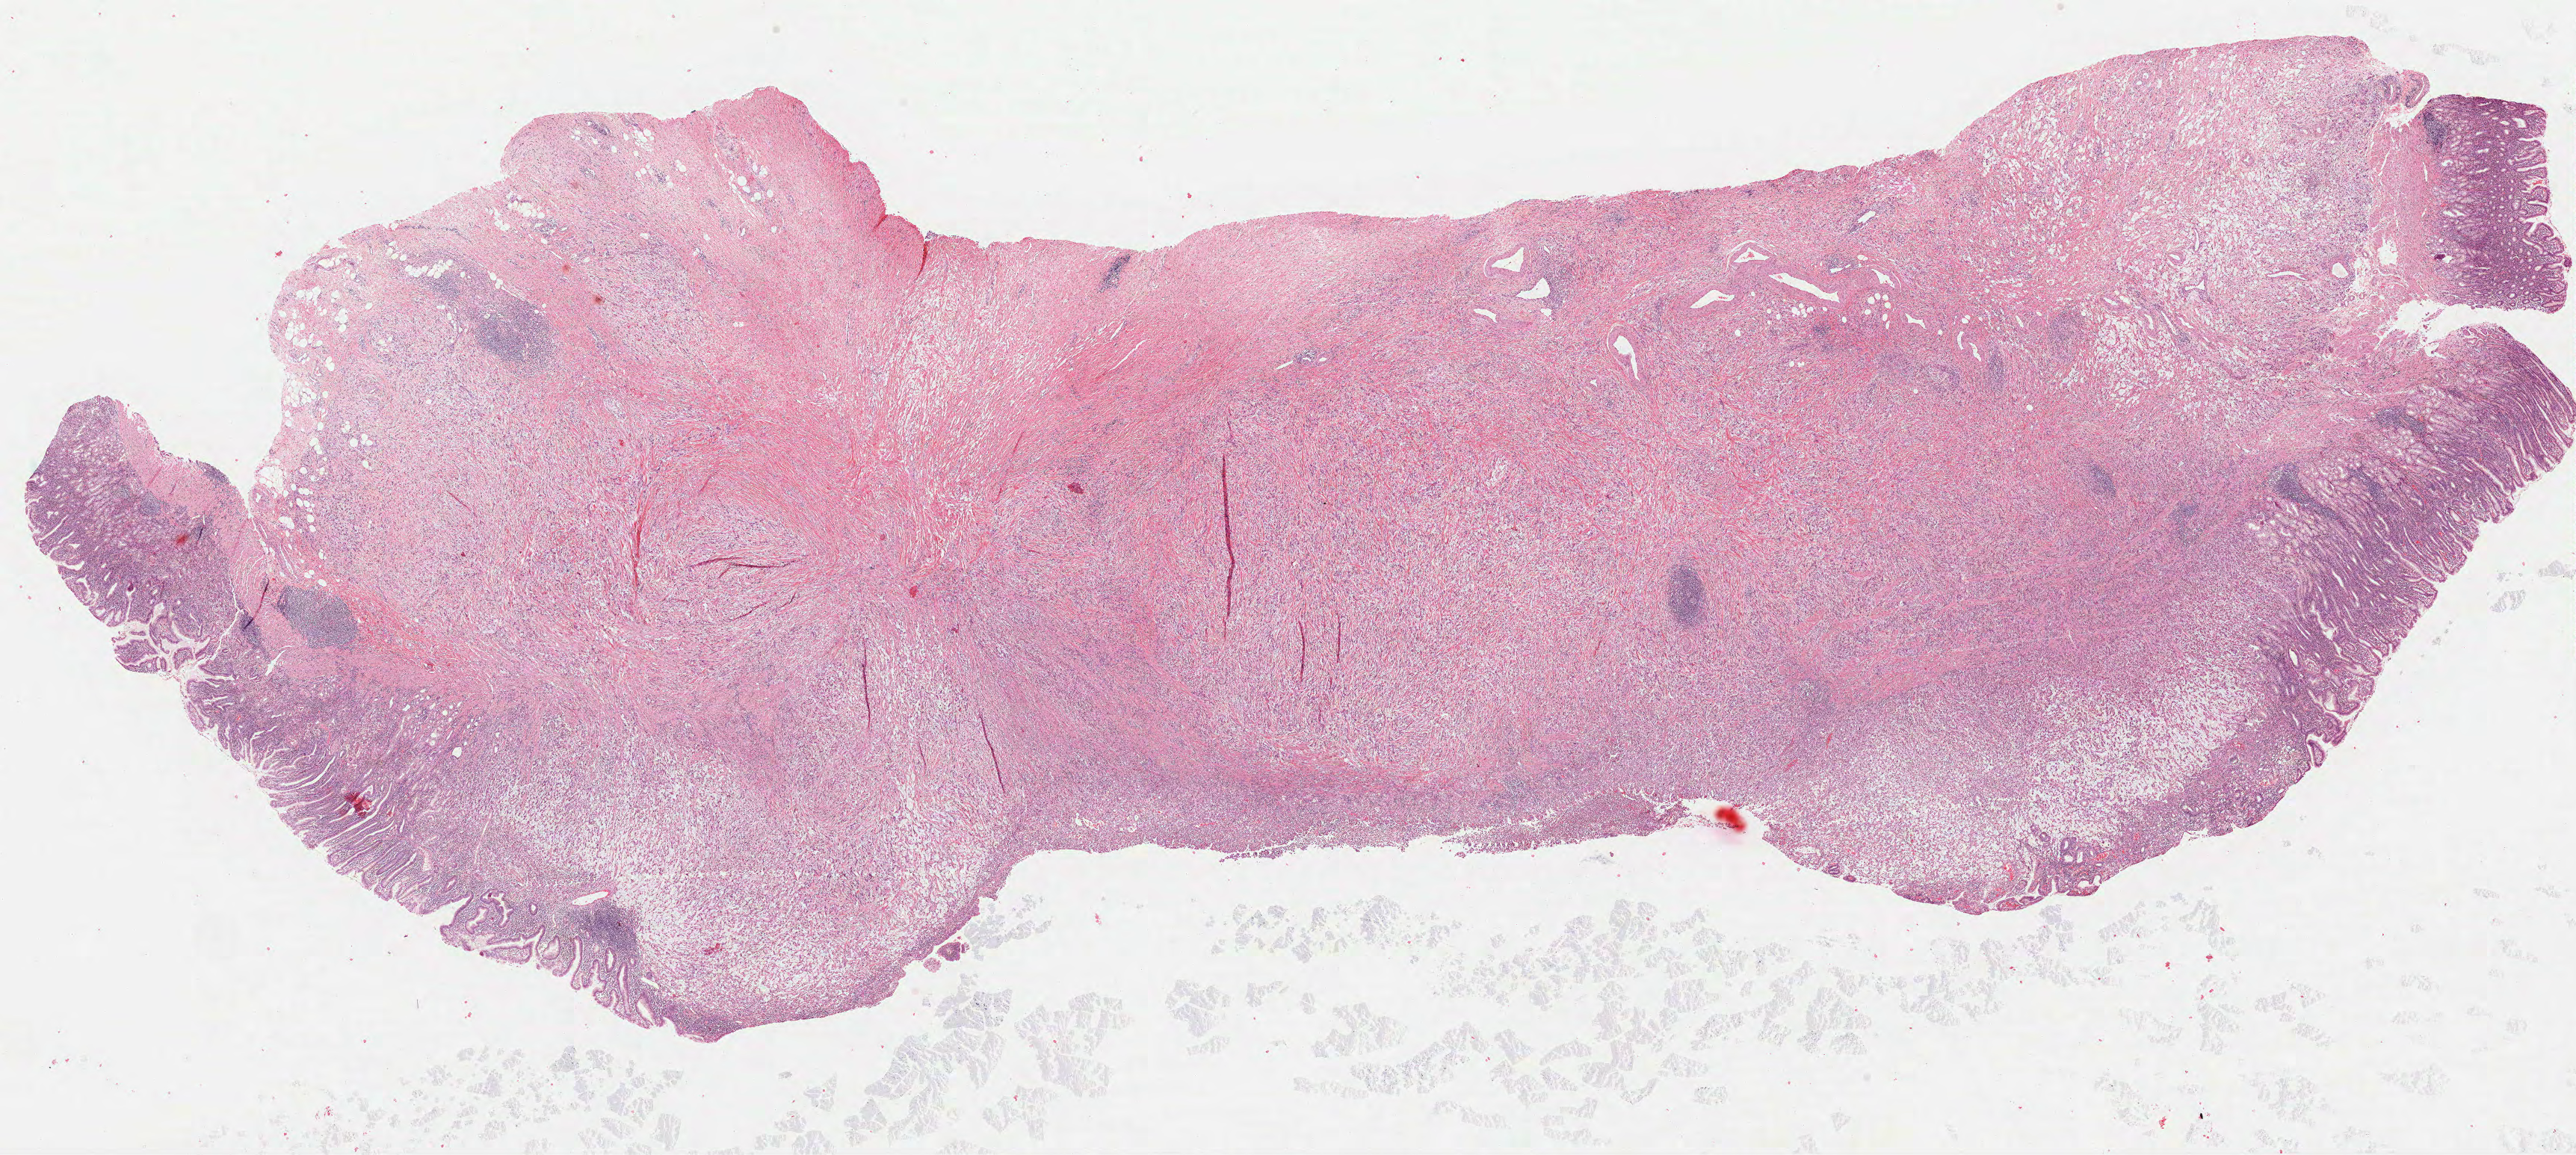
Digitized Hematoxylin and eosin (H&E) stained tissue section (whole slide), whole scanned area (about 27.8 x 12.5 mm, slide scanned at 40x) shown as a low-resolution overview; formalin-fixed paraffin-embedded (FFPE) diagnostic section; sample: primary tumour, stomach. Male, age 60 years at initial diagnosis. Histologic grade: G3 (poorly differentiated).
Lymph nodes positive (case pathology): 1 of 3 examined. AJCC pathologic stage: IIB (7th edition). Pathologic diagnosis: Adenocarcinoma, NOS (gastric antrum).